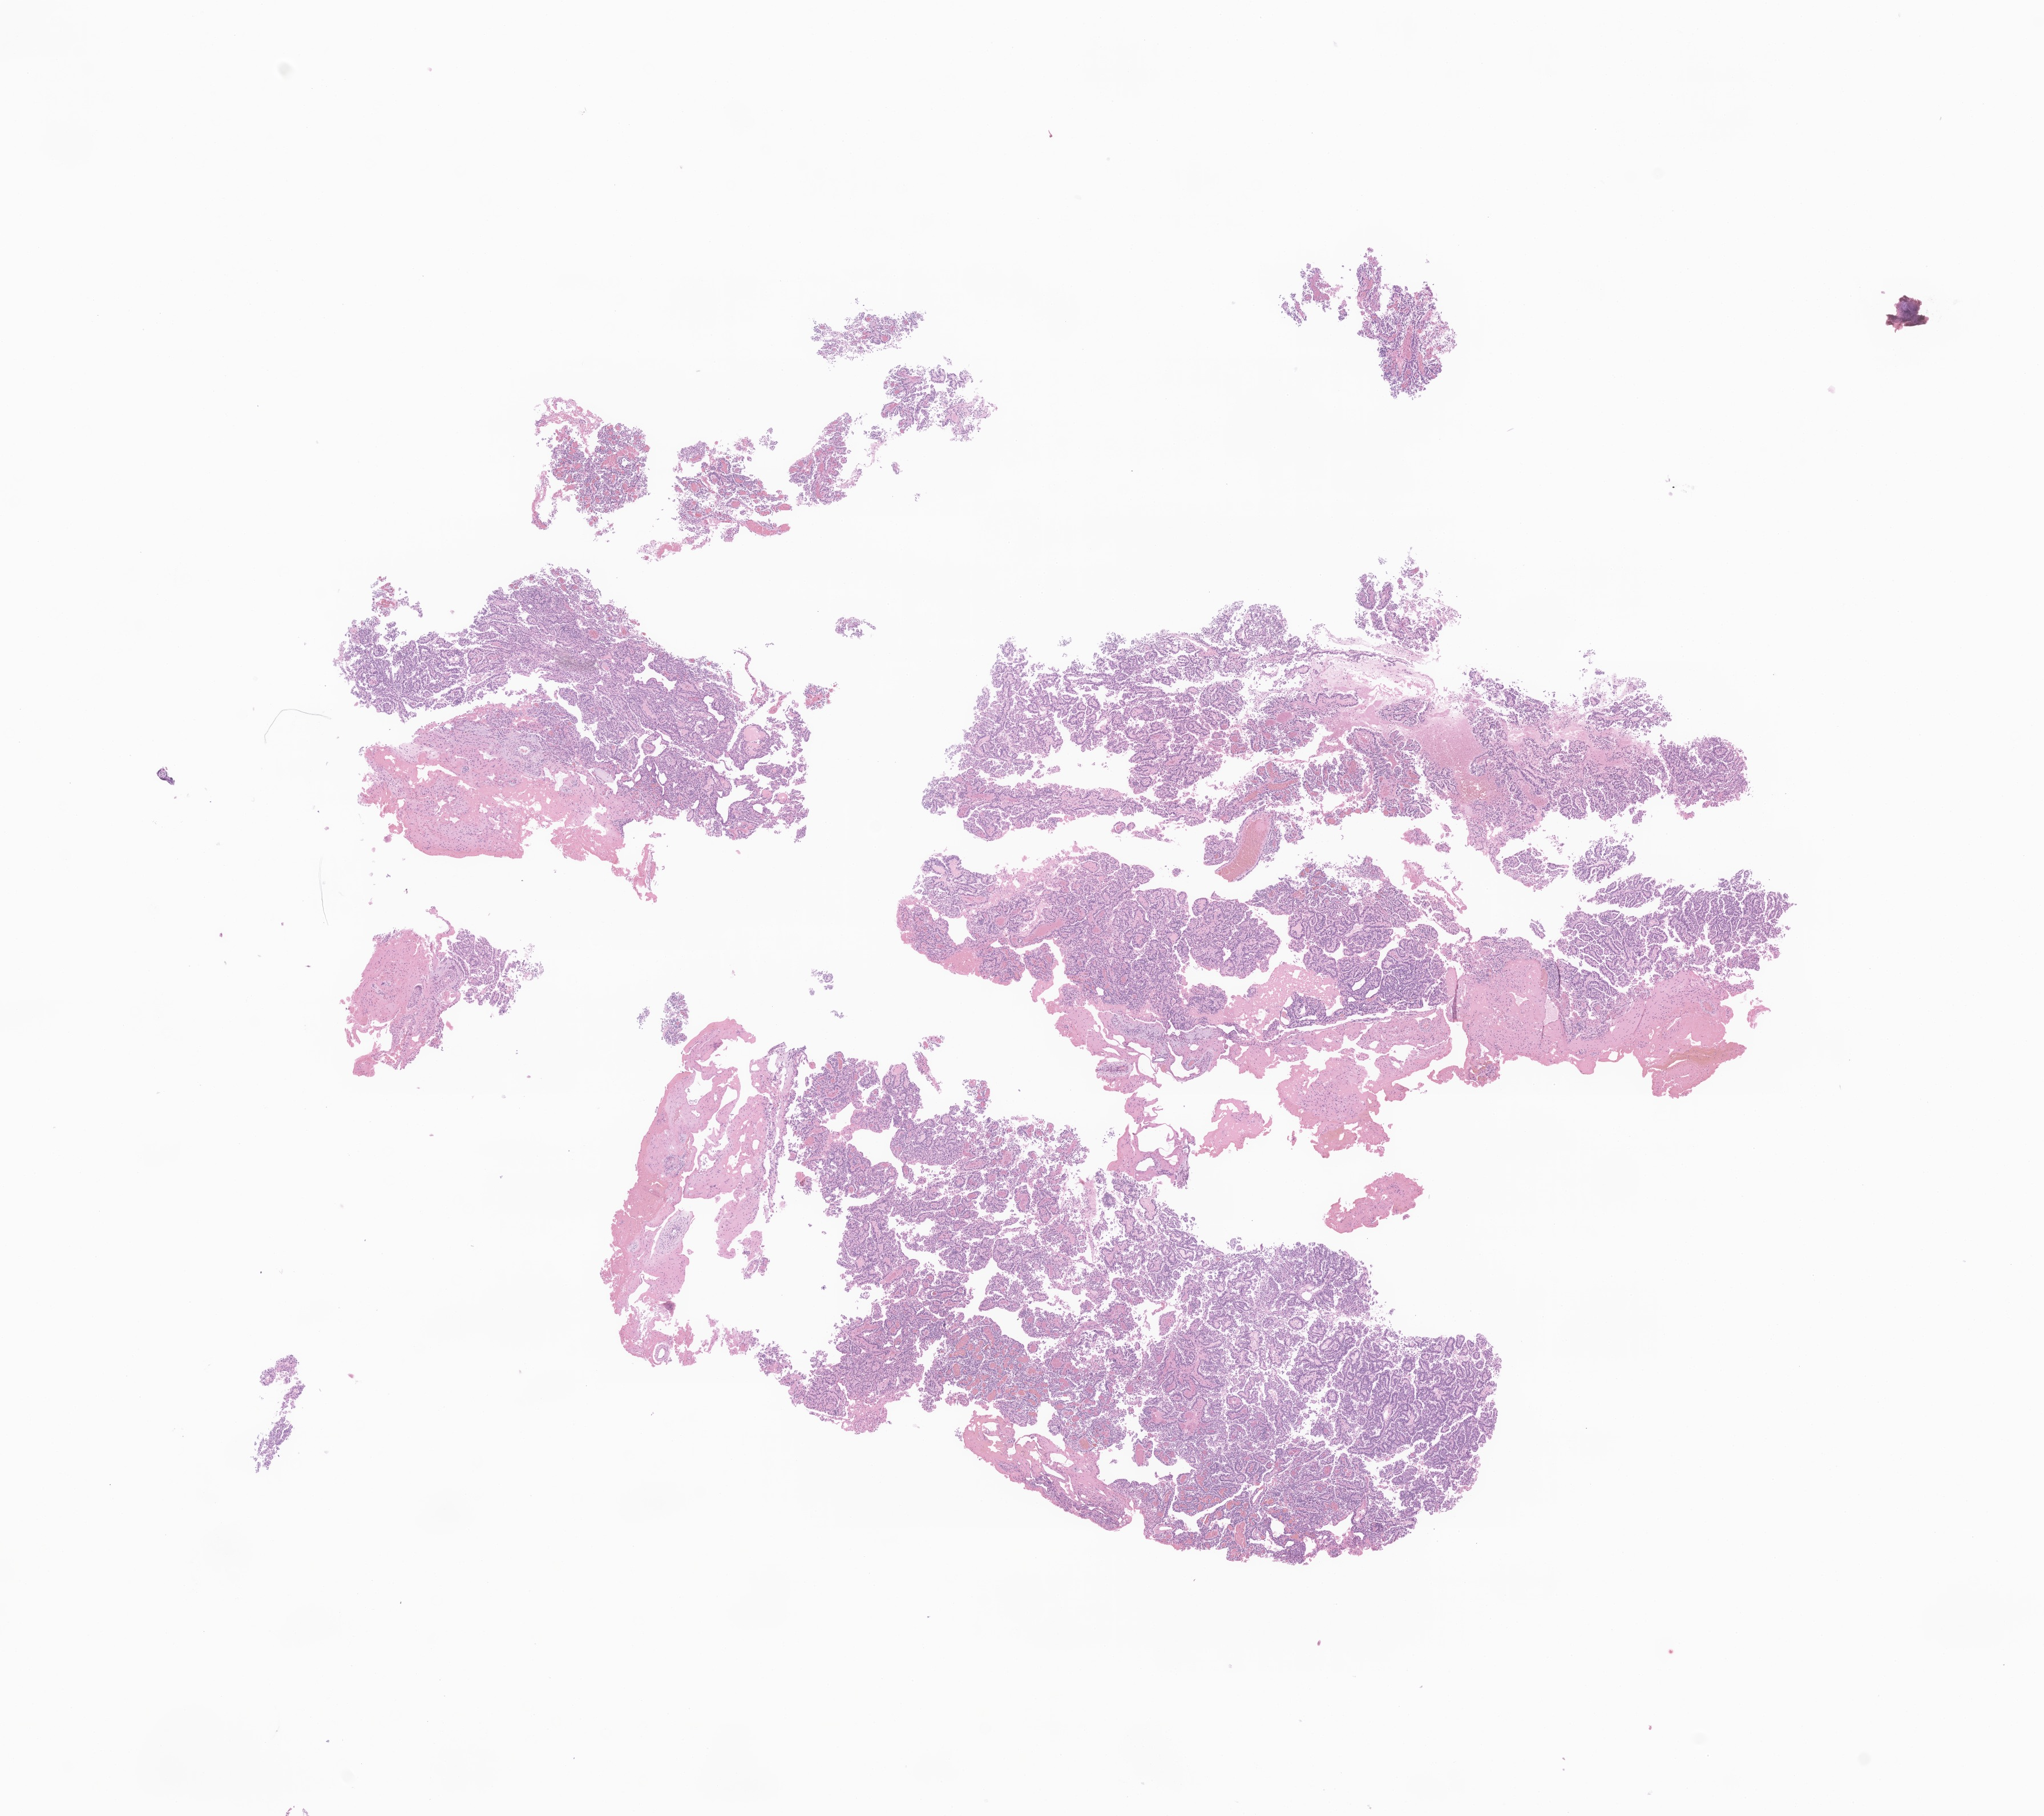
Whole-slide image, haematoxylin and eosin stain of tumor tissue from the brain — whole scanned area (about 15.1 x 13.4 mm) shown as a low-resolution overview, formalin-fixed, paraffin-embedded (FFPE) tissue. Patient male; age 840 days (about 2.3 years).
• recorded diagnosis: Choroid plexus papilloma, NOS